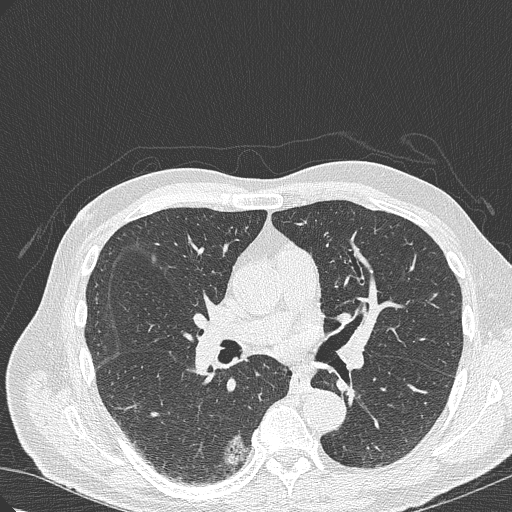
Axial slice from a low-dose chest CT screening exam. Baseline screening round. Lung window (W 1500 / L -600 HU). Lung (sharp) reconstruction kernel (B50f). 512 × 512 image matrix. Male participant, aged 70 years at enrolment. Current smoker at enrolment.
Lesion marked by an expert reader, bounding box [x1, y1, x2, y2] px = [198, 419, 261, 478]. The screening reader recorded 4 non-calcified nodules or masses ≥4 mm on this exam; which of them this box marks is not recorded. Later outcome: lung cancer diagnosed 978 days after this screen (after the third annual screen) — bronchiolo-alveolar adenocarcinoma, NOS, right lower lobe, poorly differentiated (G3), stage IB (AJCC 6th edition), 30 mm at pathology.